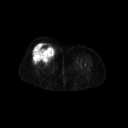
FDG PET of an extremity soft-tissue mass (from a PET/CT study), one axial slice; 3.27 mm slice thickness; 128 × 128 image matrix, field of view 700 × 700 mm. Patient: female, 56 years. From the clinical record (not read from this slice): histological type: malignant solitary fibrous tumor; grade: intermediate; site of the primary tumour: right thigh.
Outlined on this slice (expert contour drawn on MRI and transferred to this co-registered scan by the dataset authors):
- gross tumour volume including surrounding oedema: bounding box [x1, y1, x2, y2] px = [32, 42, 56, 60]
- gross tumour volume (mass): [33, 42, 55, 60]